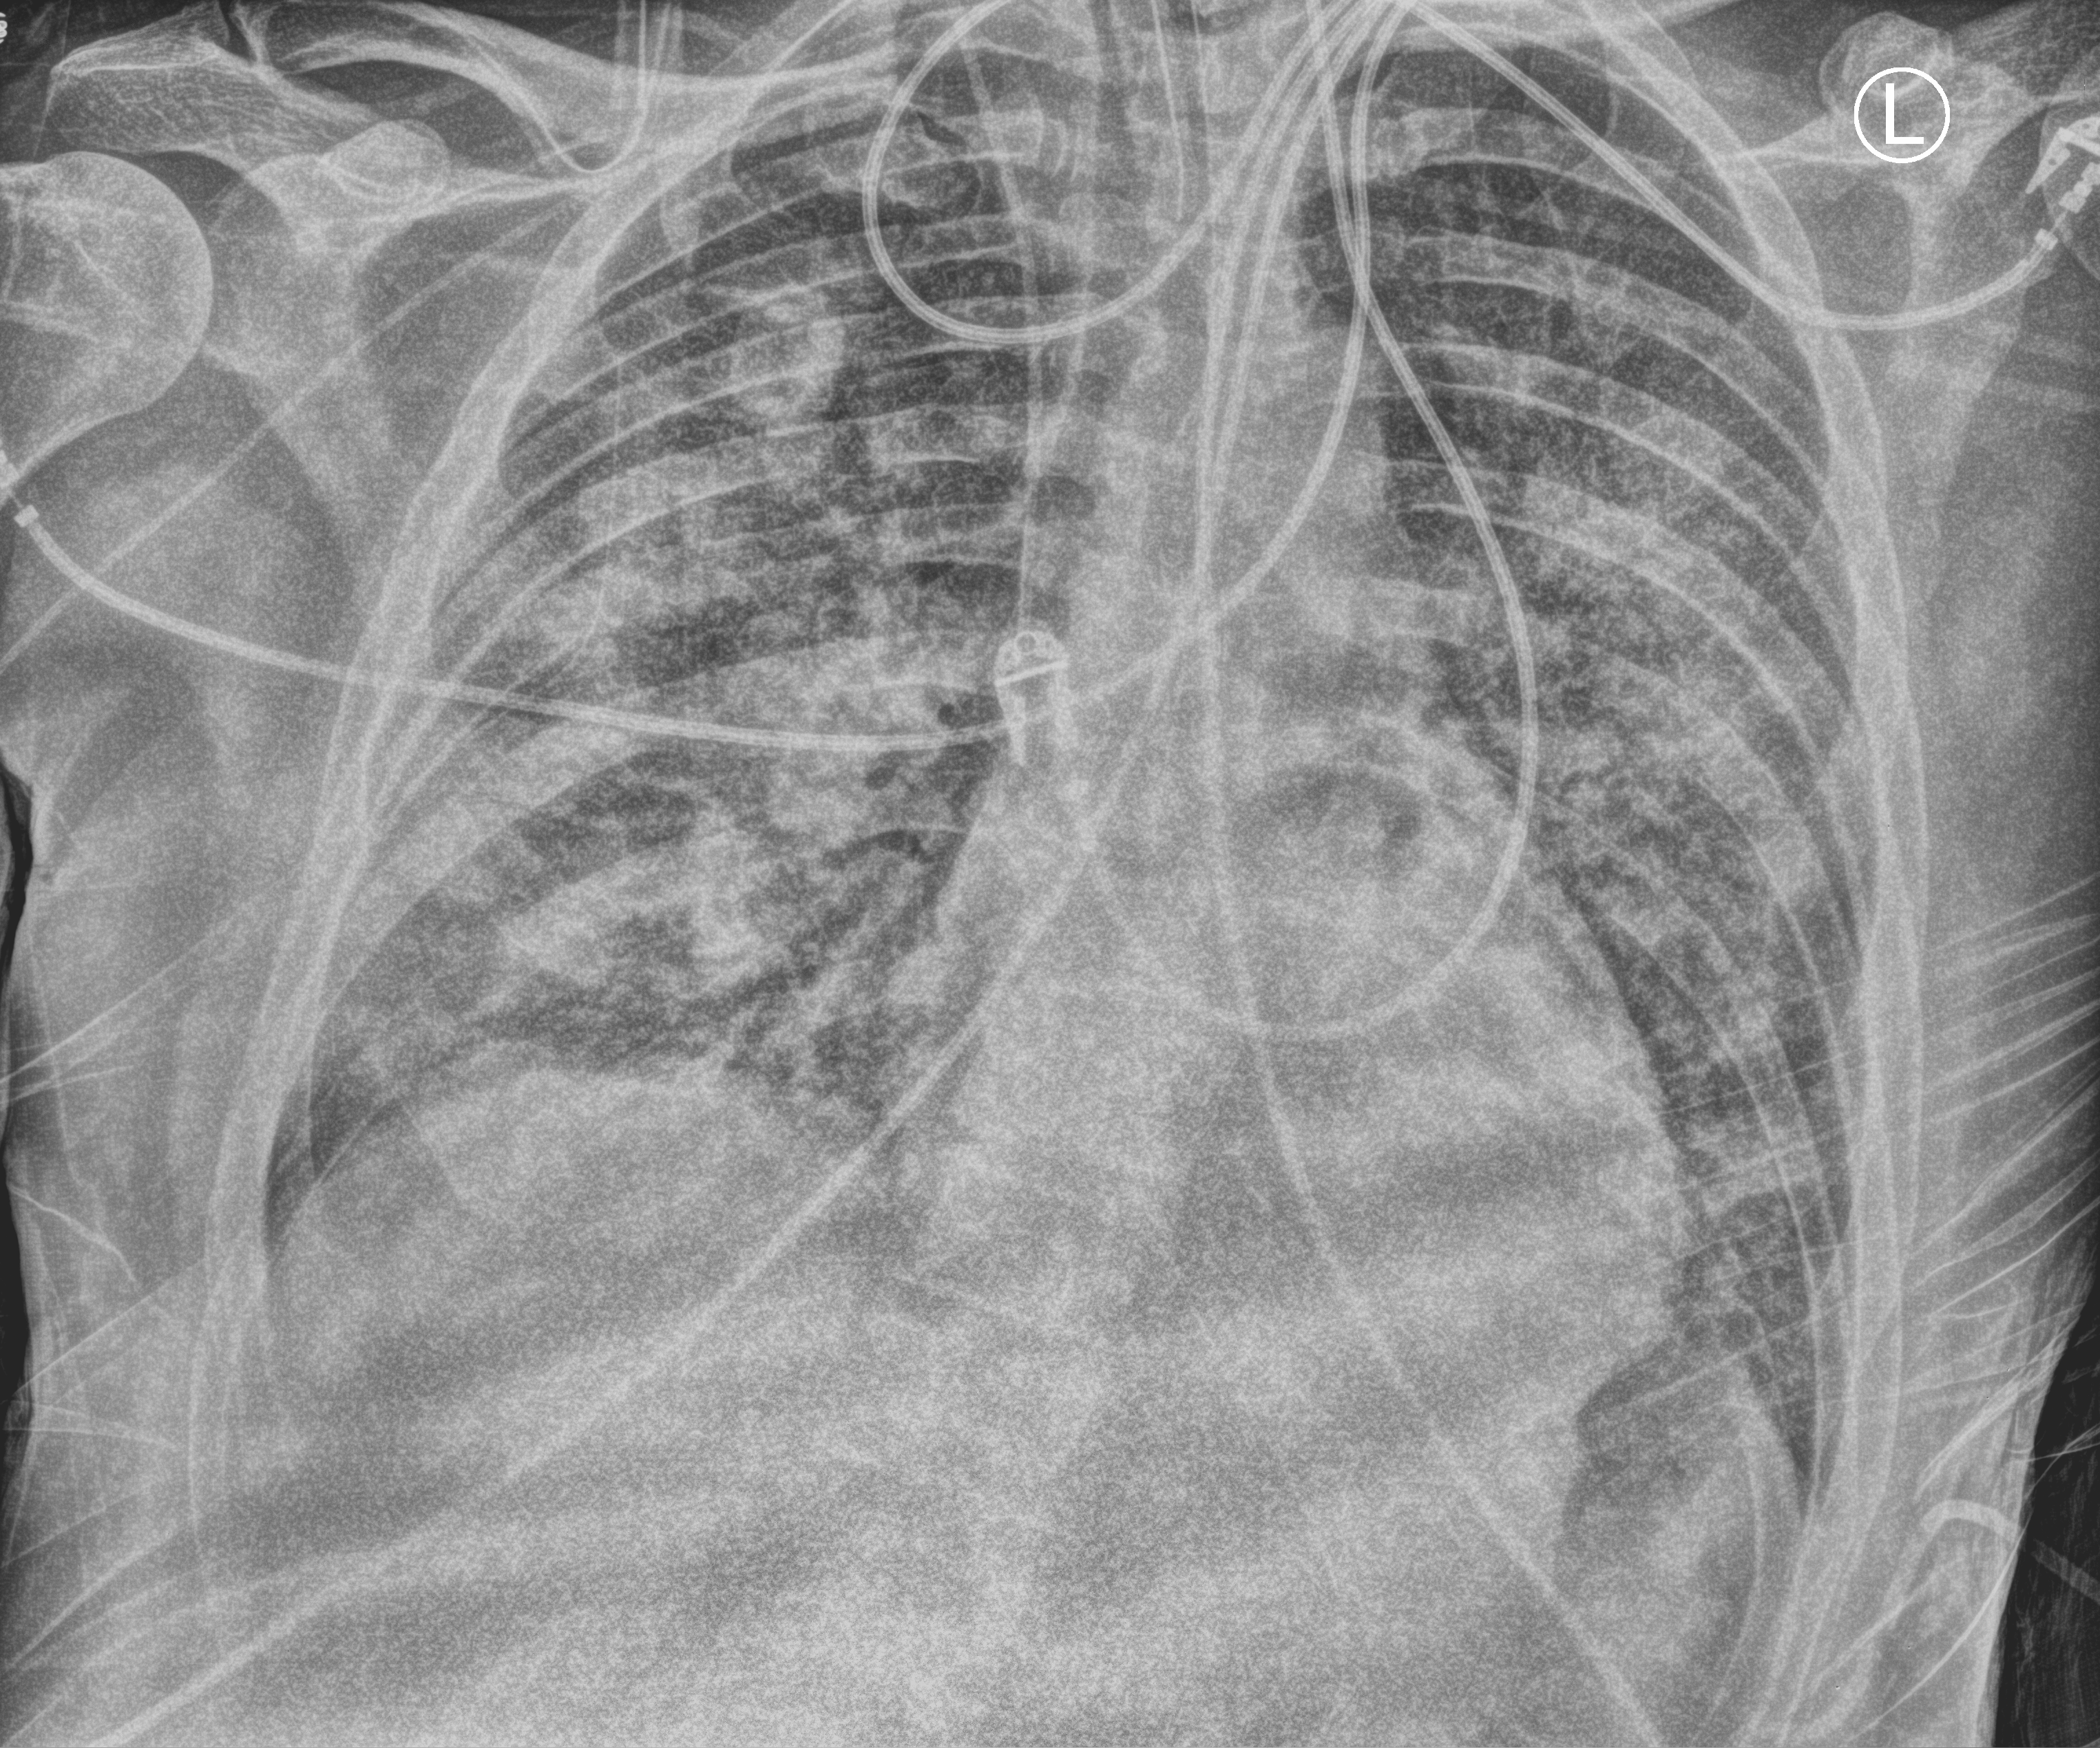
Bedside chest radiograph (computed radiography); anteroposterior (AP) projection. Patient hospitalised with COVID-19; male, aged 18–59 years.
From the hospital-stay record, not from the radiograph (when in the stay this image was taken is not recorded): mechanically ventilated during this hospital stay: yes.